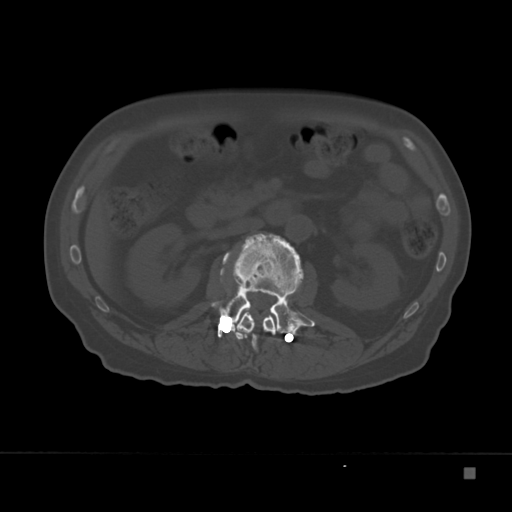
CT including the spine, one axial slice. Slice 97 of 332 in the series (ordered by position). Reconstruction kernel Br40s. Bone window (W 1800 / L 400 HU). 1.5 mm slice thickness. 512 × 512 image matrix, field of view 389 × 389 mm. Male patient, age 72 years. Case-level facts recorded for this patient, not image findings: primary cancer: skeletal.
Outlined on this slice (semi-automatic segmentation, software-assisted and operator-edited):
- L1 vertebra: bounding box [x1, y1, x2, y2] px = [233, 308, 277, 352]
- L2 vertebra: [211, 237, 315, 337]